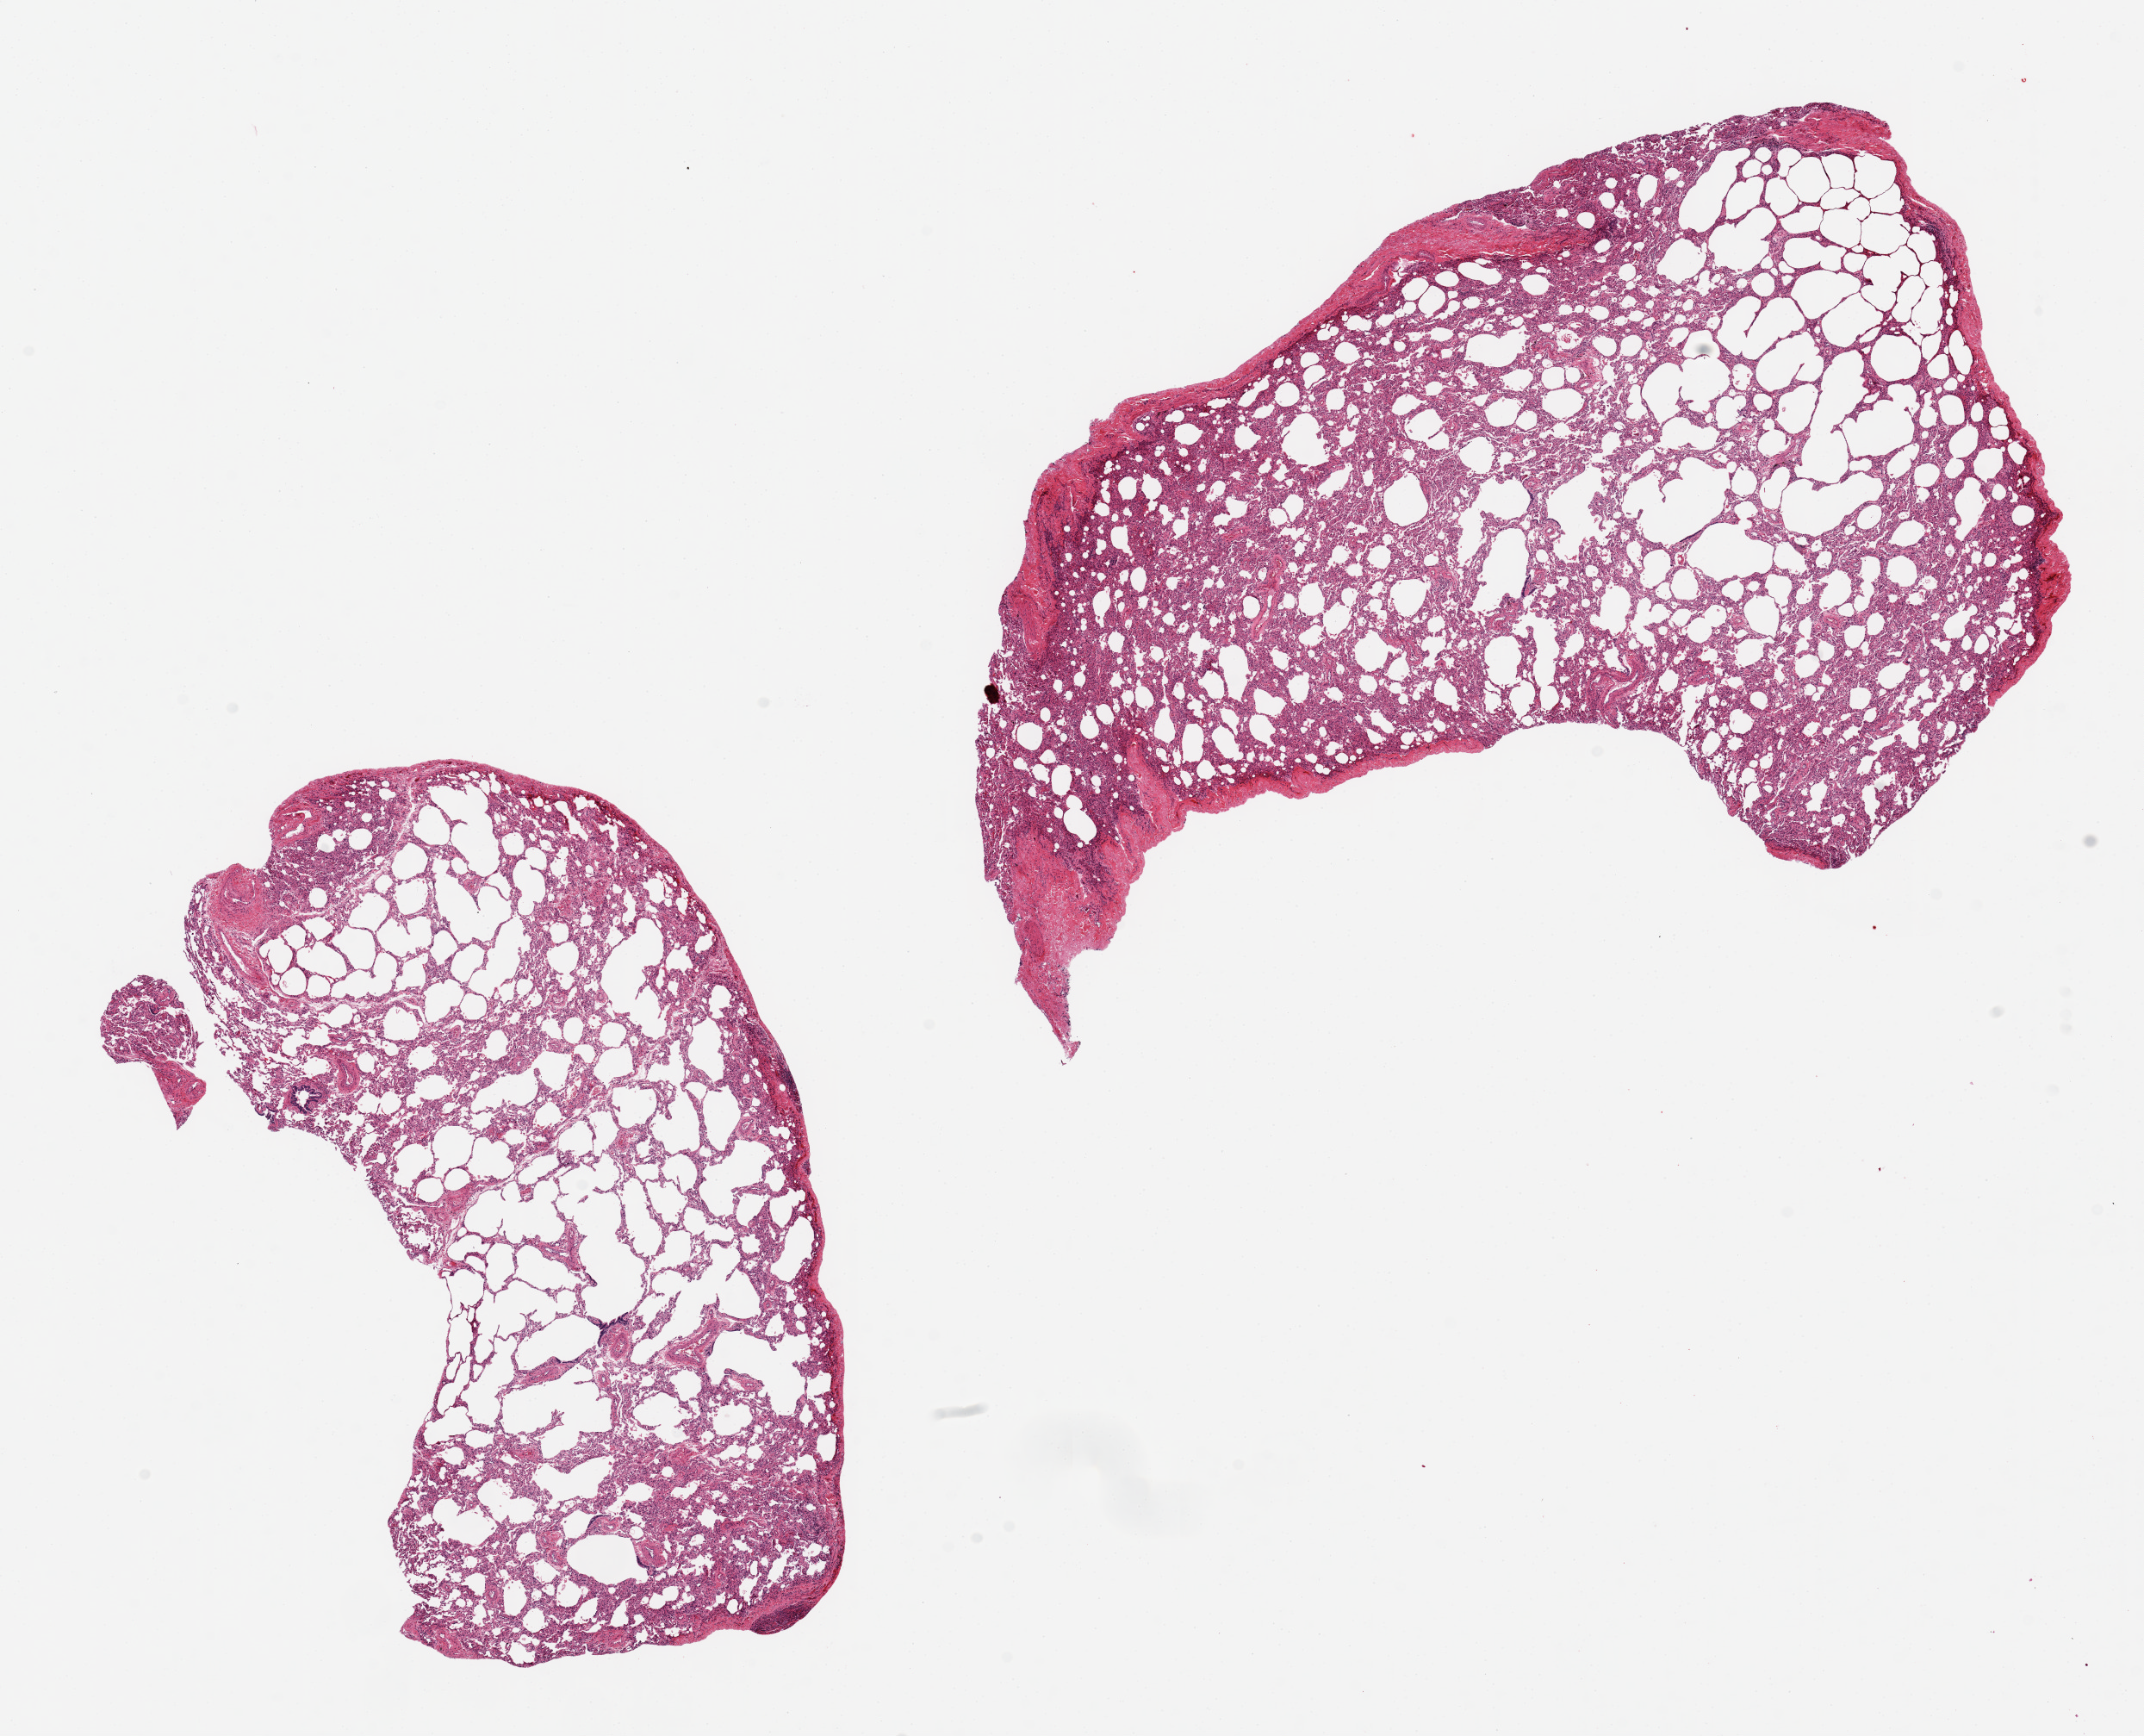
Haematoxylin and eosin whole-slide image, a low-resolution overview of the entire scanned area, about 19.7 x 15.9 mm (slide scanned at 20x). PAXgene-fixed, paraffin-embedded tissue. Sampled site (target tissue): lung. Donor tissue sample. Donor sex: male.
Reviewer comment on this tissue sample: 2 pieces, 10x7 & 8x5 mm; patchy emphysema.